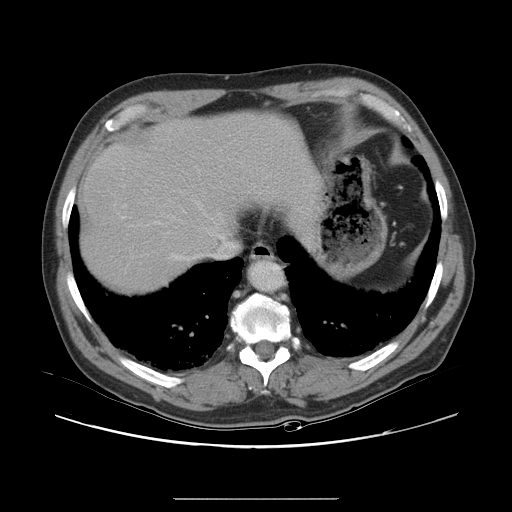
Contrast-enhanced abdominal CT, one axial slice; slice 27 of 40 in the series (ordered by position); soft-tissue window (W 400 / L 40 HU); 5 mm slice thickness; 512 × 512 image matrix, field of view 408 × 408 mm. Male patient, age 64 years. Case-level facts recorded for this patient, not image findings: diagnosis: colorectal cancer liver metastases, imaged before liver resection; multiple liver metastases: yes; largest metastasis: 3.2 cm; disease in both lobes: yes.
Annotated regions visible in this slice (expert manual segmentation):
- hepatic veins: box from (x=123, y=205) to (x=224, y=261) px
- liver: (x=83, y=115)–(x=311, y=292)
- planned liver remnant (the part of the liver to remain after resection): (x=83, y=115)–(x=310, y=269)
- portal vein (with intrahepatic branches): (x=122, y=217)–(x=124, y=219)